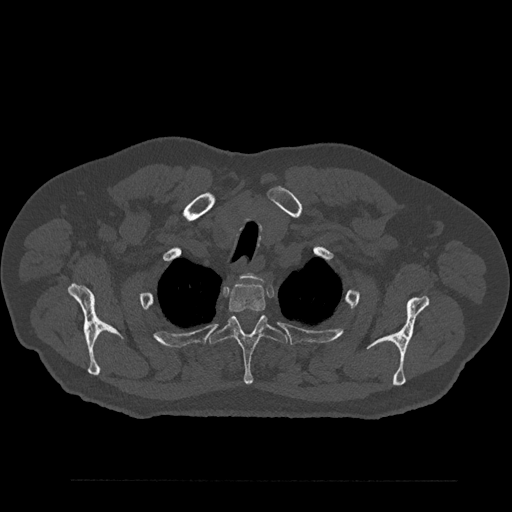
CT including the spine, one axial slice; position 699 of 797 along the scan axis; reconstruction kernel Br40s/3; 120 kVp; bone window (W 1800 / L 400 HU); 512 × 512 image matrix, field of view 430 × 430 mm. Patient: male, 61 years. From the clinical record (not read from this slice): primary cancer: prostate.
Outlined on this slice (semi-automatically segmented with operator editing):
- T1 vertebra: bounding box <243,274,256,278> (left, top, right, bottom; pixels)
- T2 vertebra: <227,282,266,313>
- T3 vertebra: <210,315,288,385>